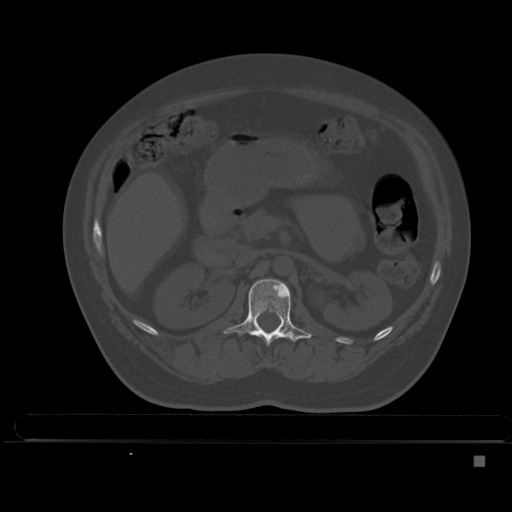
CT including the spine, one axial slice; position 195 of 495 along the scan axis; bone window (W 1800 / L 400 HU); 1.5 mm slice thickness; 512 × 512 image matrix, field of view 404 × 404 mm. Patient: female, 33 years. From the clinical record (not read from this slice): primary cancer: breast.
Outlined on this slice (semi-automatically segmented with operator editing):
- L1 vertebra: box from (x=223, y=279) to (x=312, y=345) px